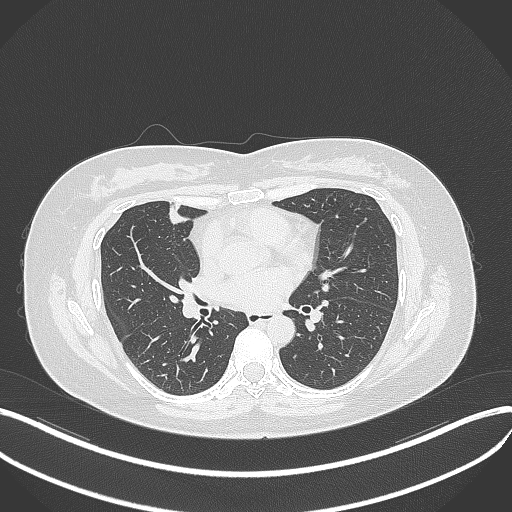
Chest CT, one axial slice. Position 159 of 273 along the scan axis. Reconstruction kernel B70f. 120 kVp. Lung window (W 1500 / L -600 HU). 512 × 512 image matrix. Patient: female, 42 years. From the clinical record (not read from this slice): clinical TNM (as recorded): T1b N0 M0.
Outlined on this slice (bounding box drawn by a radiologist):
- lung tumour (recorded histology: adenocarcinoma): bounding box <162,202,194,228> (left, top, right, bottom; pixels)